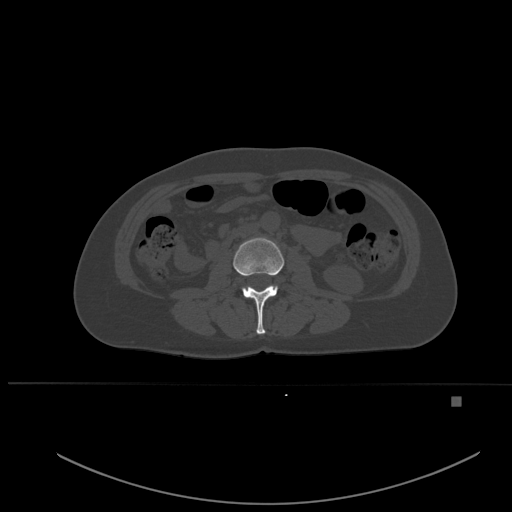
CT including the spine, one axial slice. Slice 209 of 651 in the series (ordered by position). Bone window (W 1800 / L 400 HU). 512 × 512 image matrix, field of view 443 × 443 mm. Patient: female, 49 years. From the clinical record (not read from this slice): primary cancer: breast.
Outlined on this slice (semi-automatically segmented with operator editing):
- L2 vertebra: bounding box <233,238,285,334> (left, top, right, bottom; pixels)